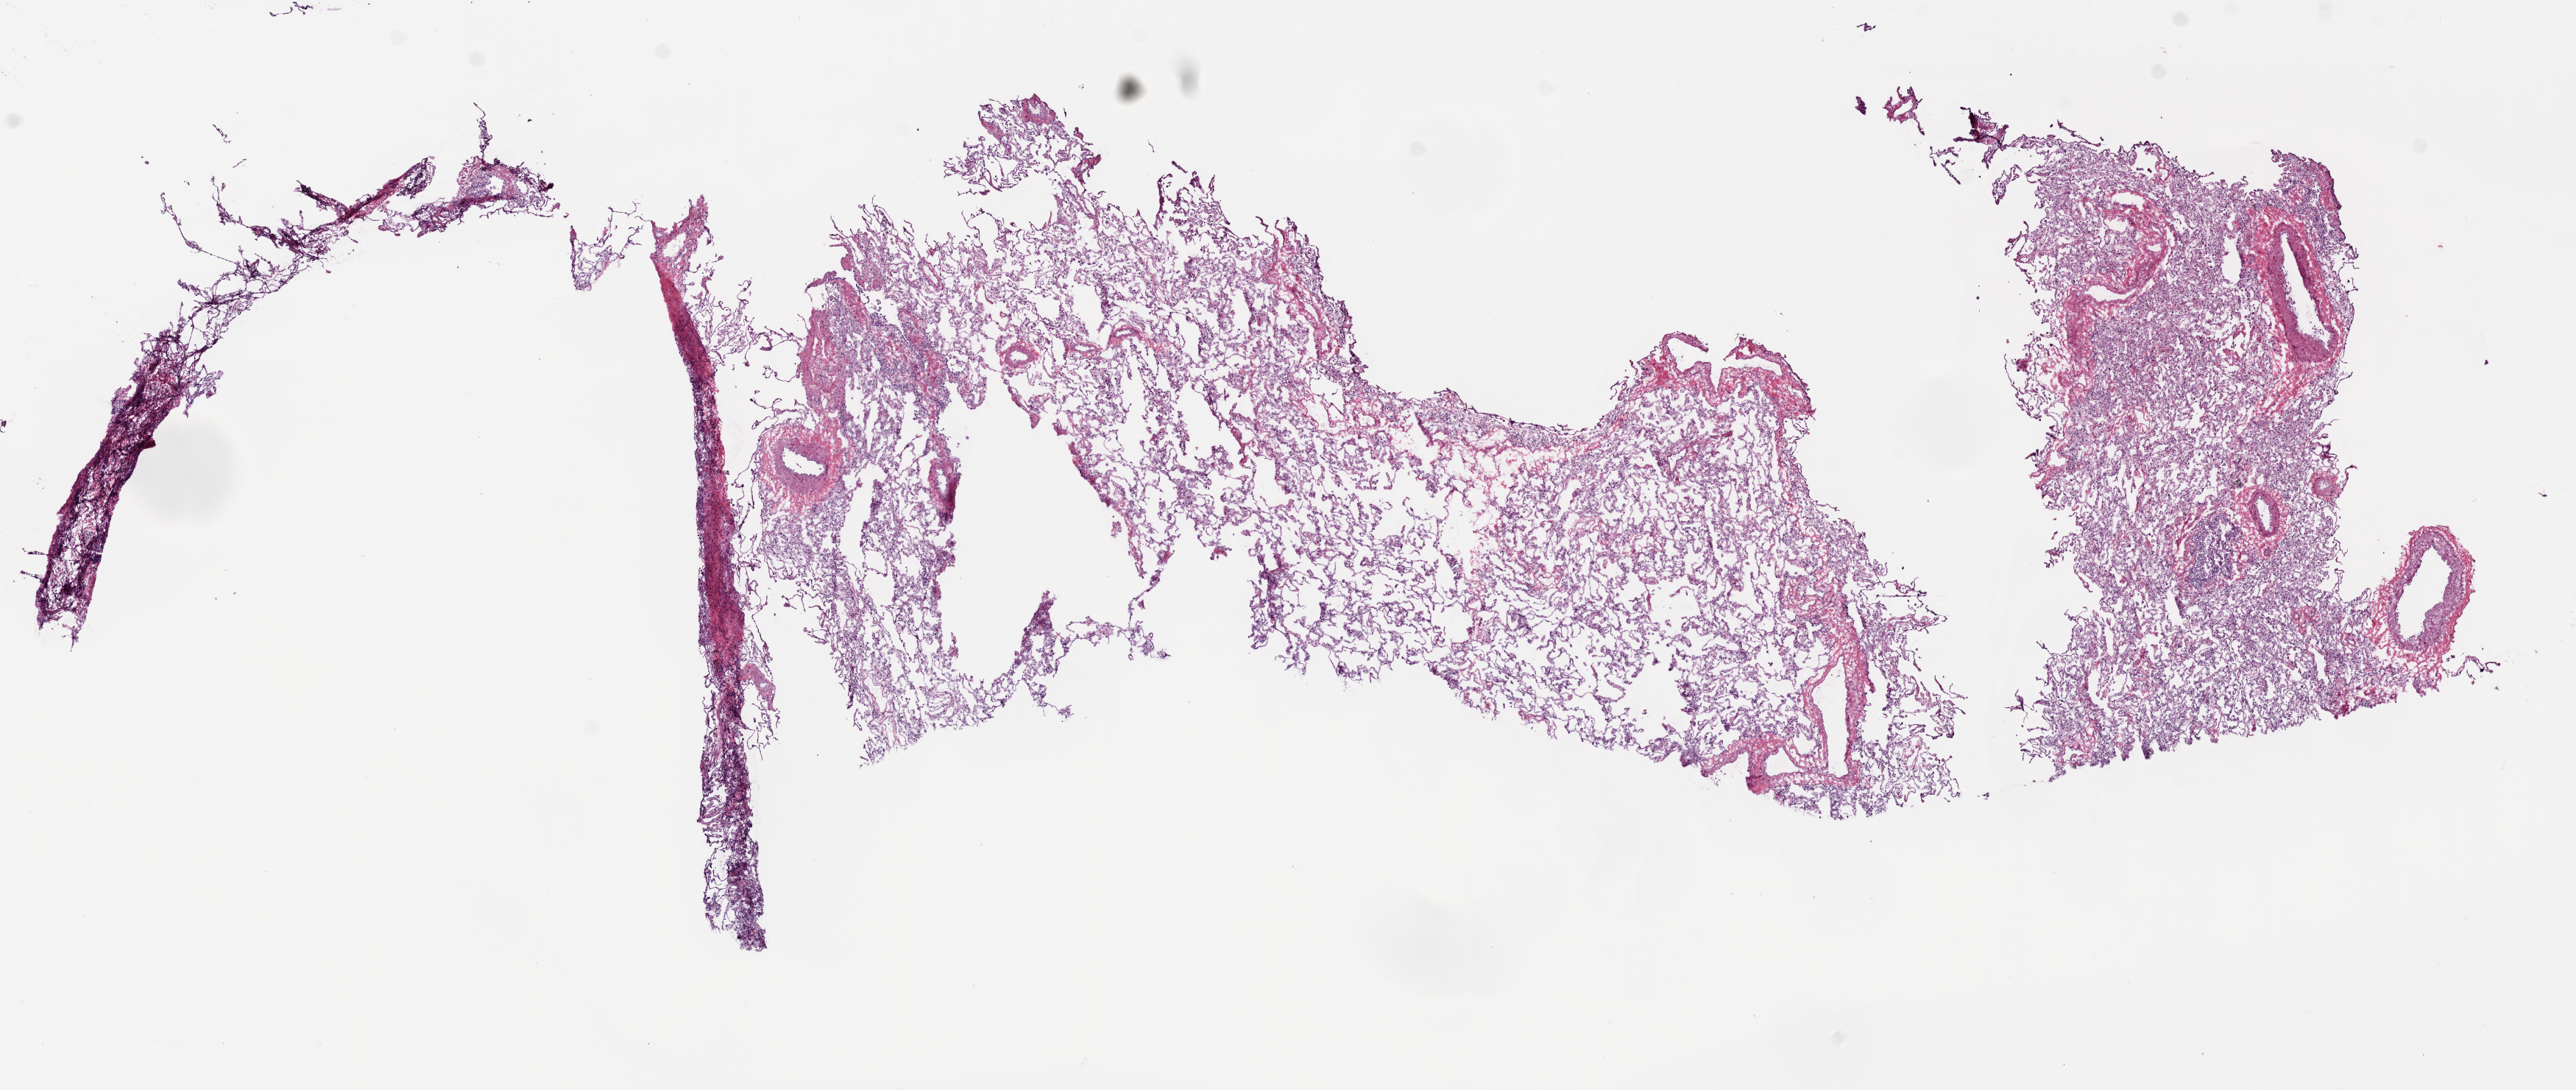
Digitized H&E tissue section (whole slide) — low-resolution overview of the scanned area, about 14.0 x 5.9 mm (from a 20x scan). Frozen section. Lung, solid tissue normal (non-tumour tissue) sample. Patient: male, age at initial diagnosis 57 years.
This section: solid tissue normal sample (biorepository sample class). Patient diagnosis: Squamous cell carcinoma, NOS (lower lobe, lung).